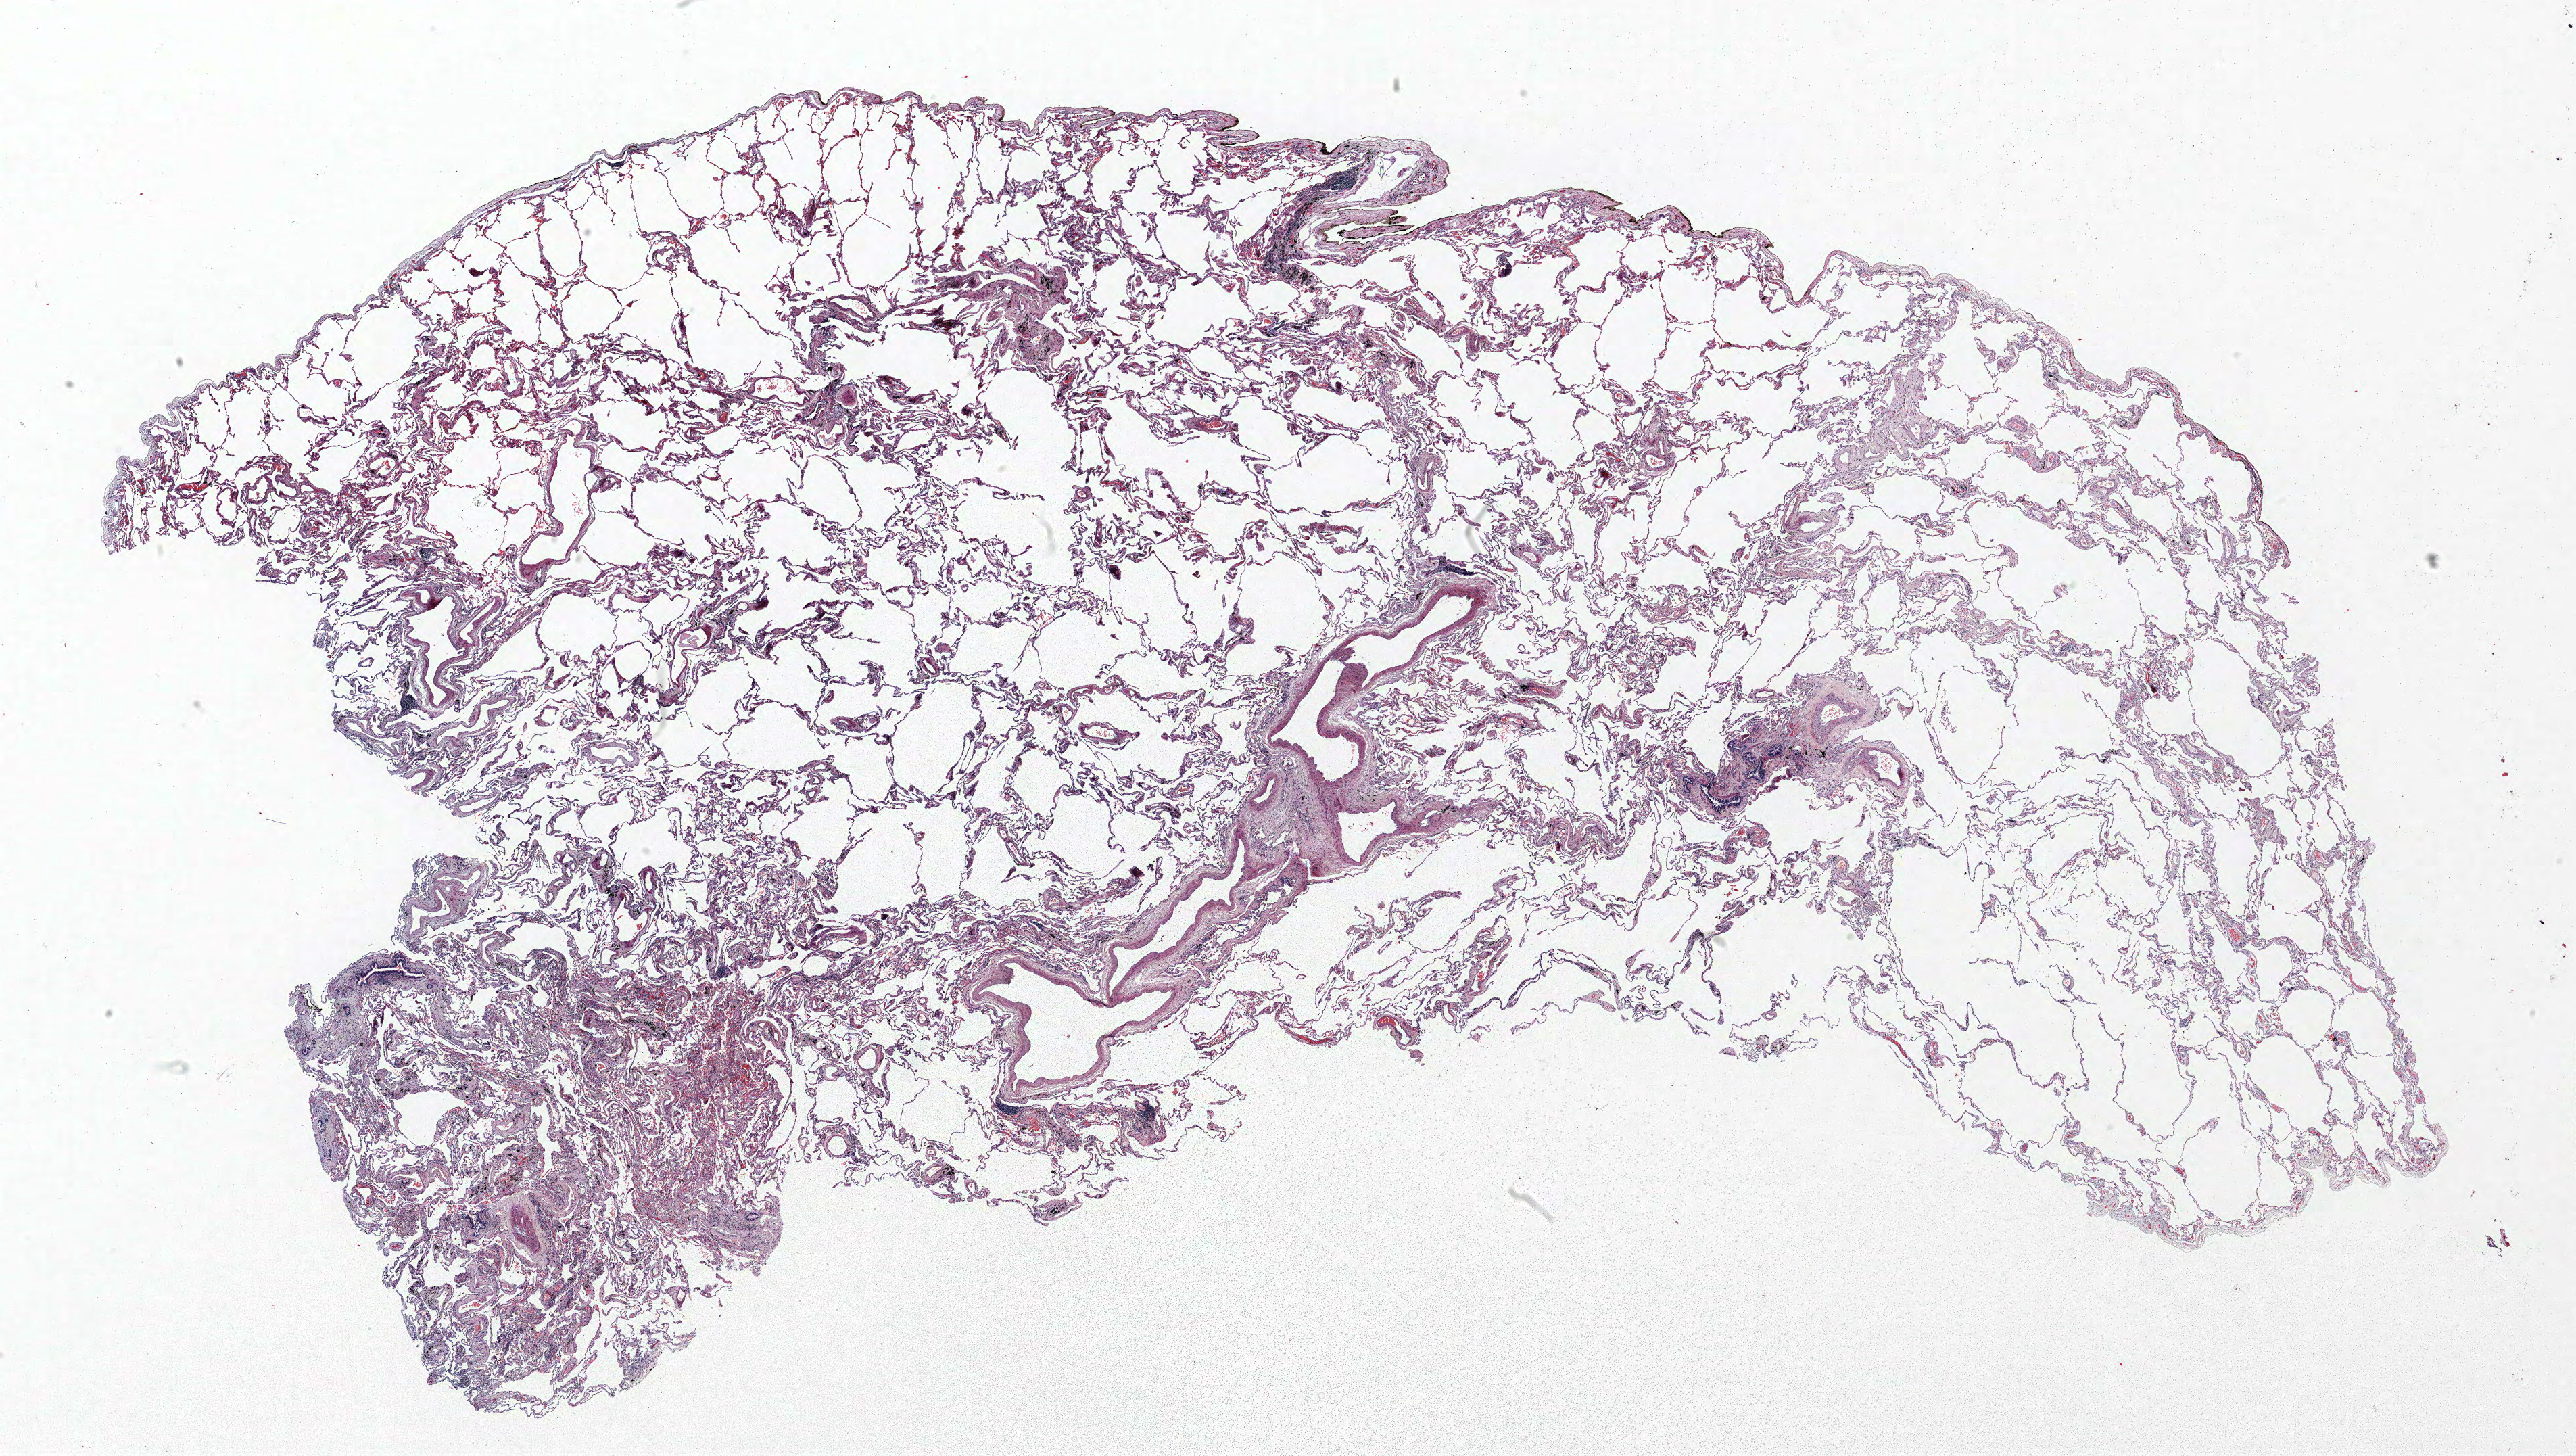
Whole-slide histology image, H&E — whole scanned area (about 30.5 x 17.2 mm, slide scanned at 40x) shown as a low-resolution overview, FFPE section, lung tissue. Female, age 60 at enrolment. Current smoker at enrolment. Grade: well differentiated (G1).
Participant's lung-cancer diagnosis: Adenocarcinoma, NOS (ICD-O-3 8140/3). Stage (AJCC 6th edition): IA. Primary tumour location (clinical record): left lower lobe. Tumour size (pathology): 15 mm.